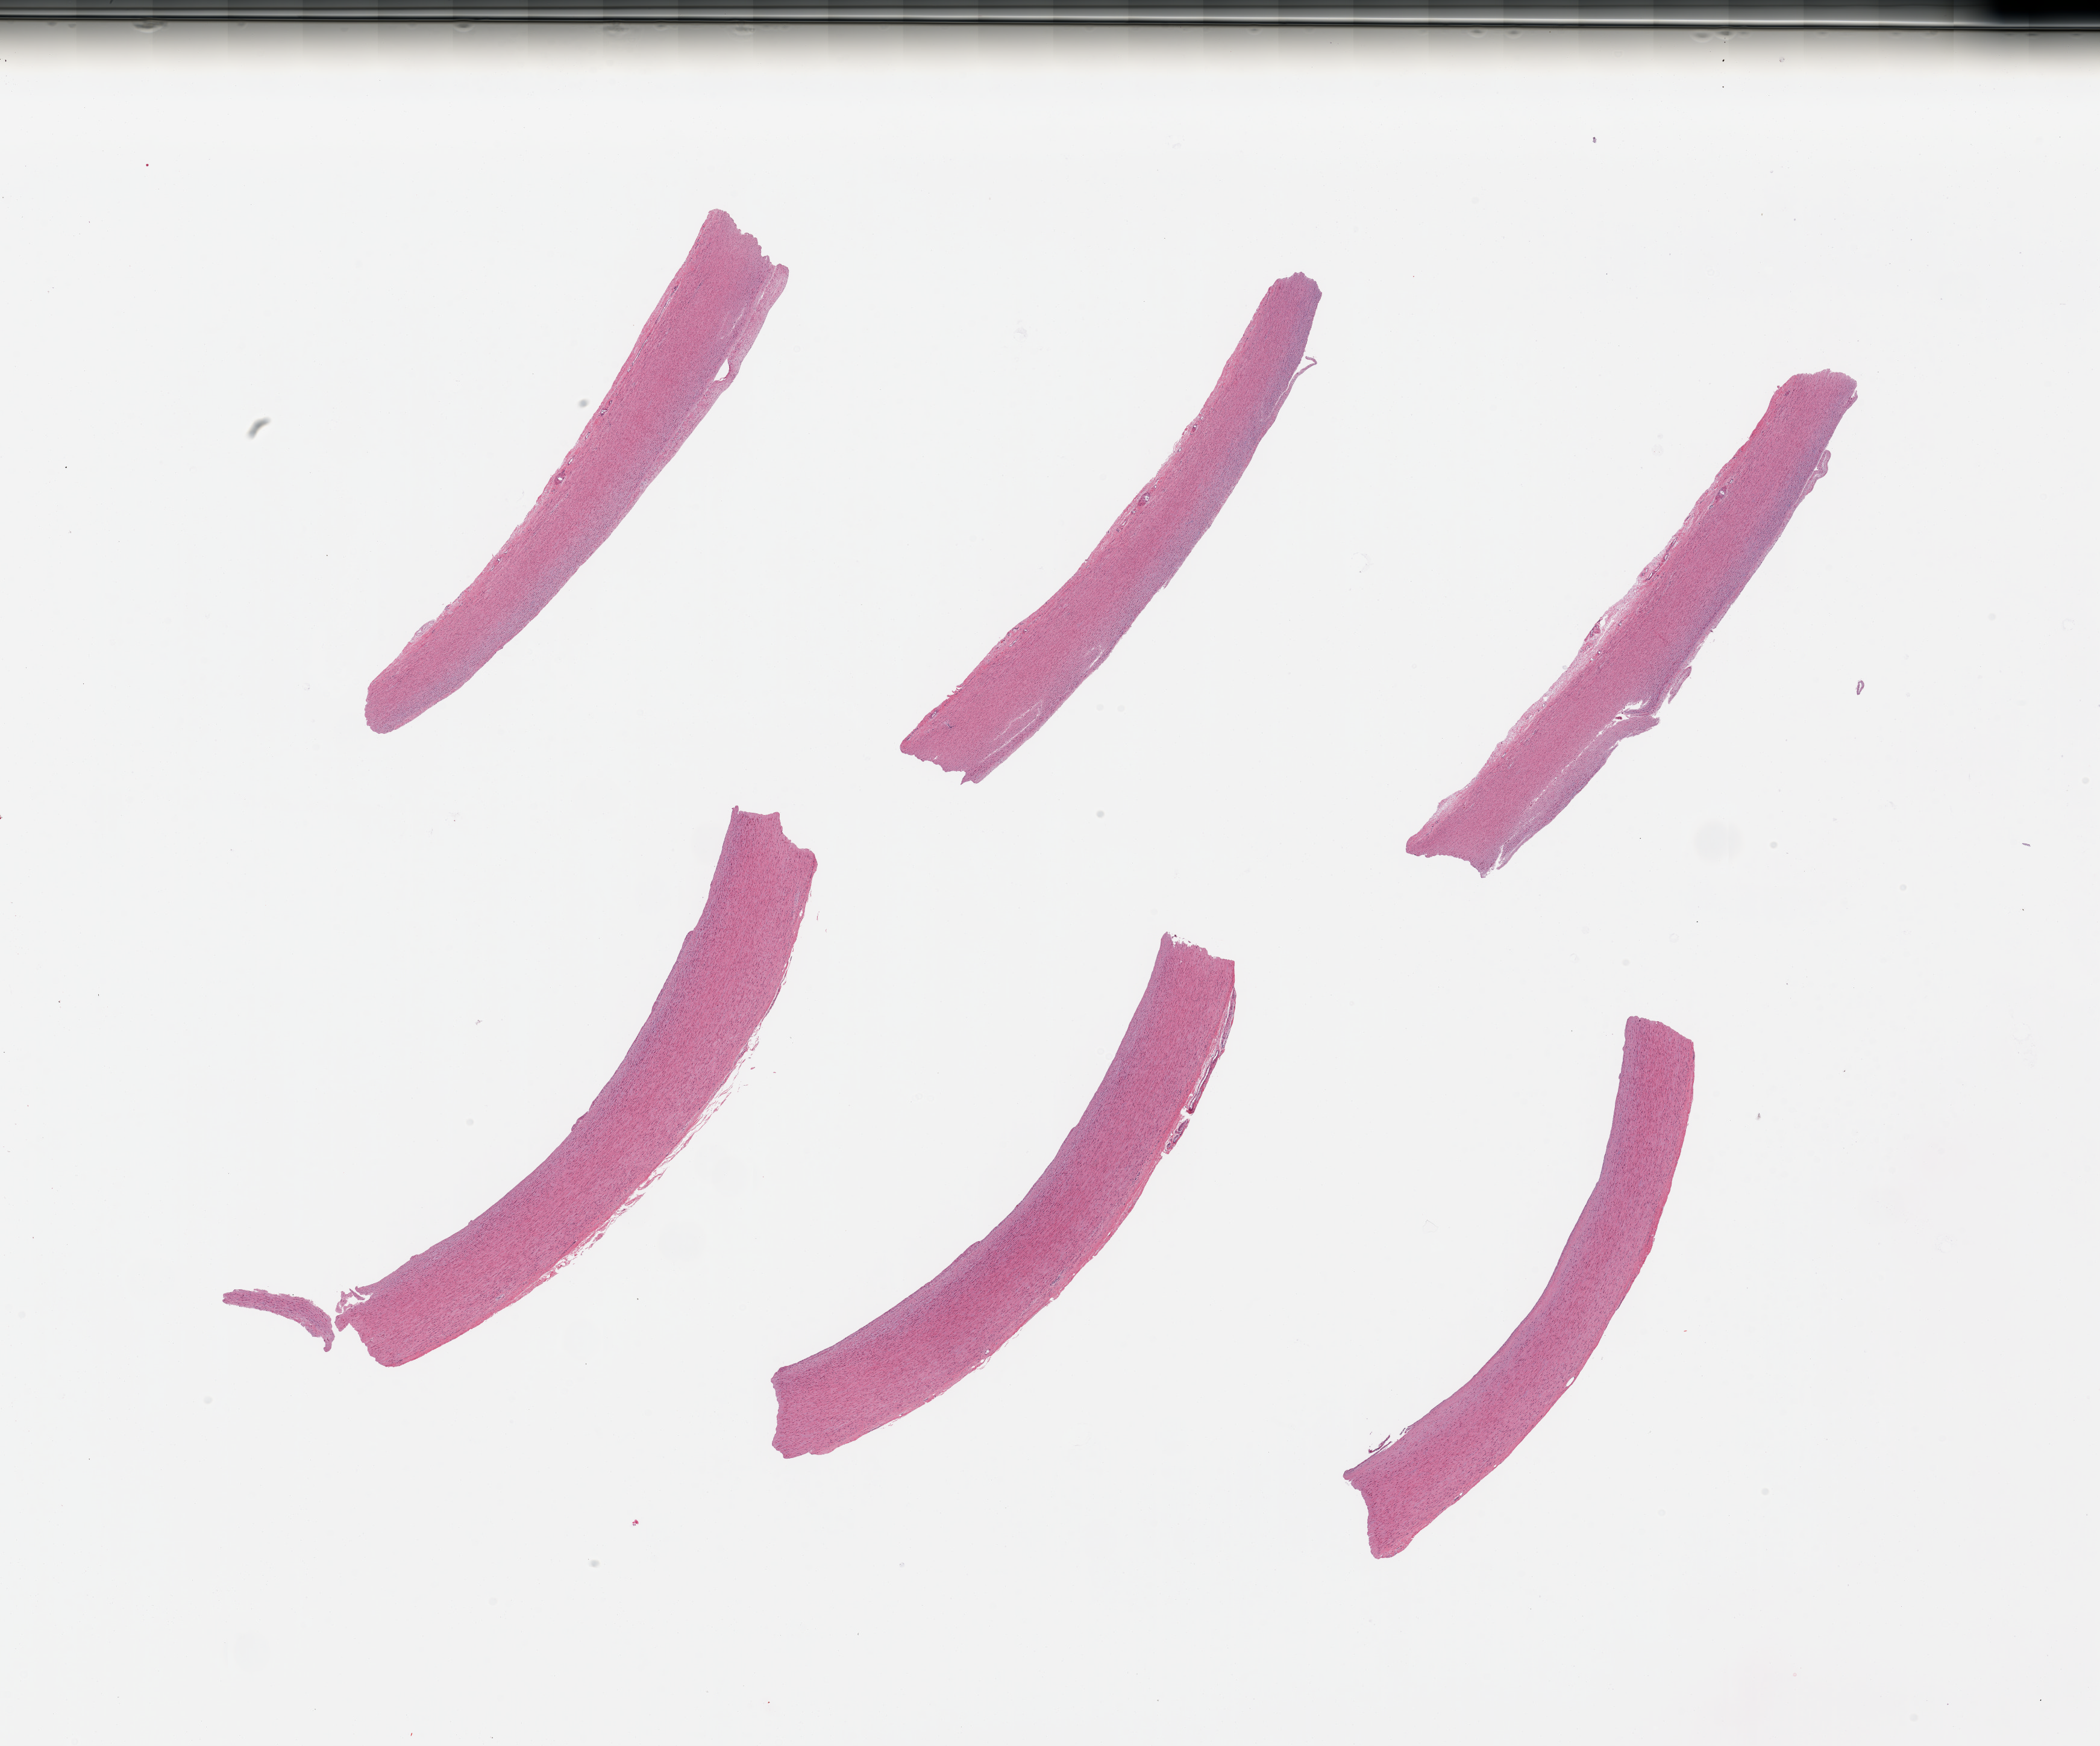
Whole-slide image, haematoxylin and eosin stain, shown as a low-resolution overview of the whole scanned area (about 27.6 x 22.9 mm), PAXgene-fixed paraffin-embedded (PFPE) section, section of aorta (target tissue), tissue donor sample. Donor sex: female.
Reviewer comment on this tissue sample: 6 pieces; early plaque.